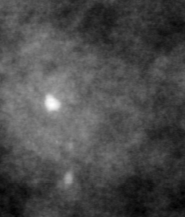
Crop from a digitized film mammogram around one marked abnormality; right breast; CC view; BI-RADS breast density category 3 (scale 1–4).
- Marked abnormality: calcifications, morphology pleomorphic, distribution clustered; BI-RADS assessment category 4; pathology result (as recorded, not read from the image): malignant.